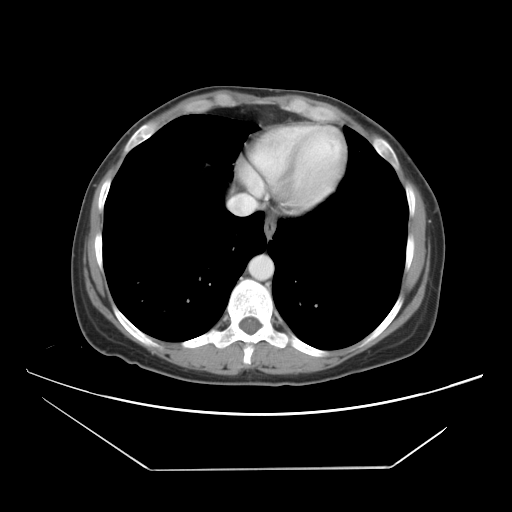
Contrast-enhanced abdominal CT, one axial slice. Position 39 of 42 along the scan axis. Soft-tissue window (W 400 / L 40 HU). 5 mm slice thickness. 512 × 512 image matrix, field of view 399 × 399 mm. Female patient, age 52 years. Case-level facts recorded for this patient, not image findings: diagnosis: colorectal cancer liver metastases, imaged before liver resection.
Structures marked on this image (manually delineated by an expert):
- hepatic veins: bounding box [x1, y1, x2, y2] px = [229, 130, 288, 215]